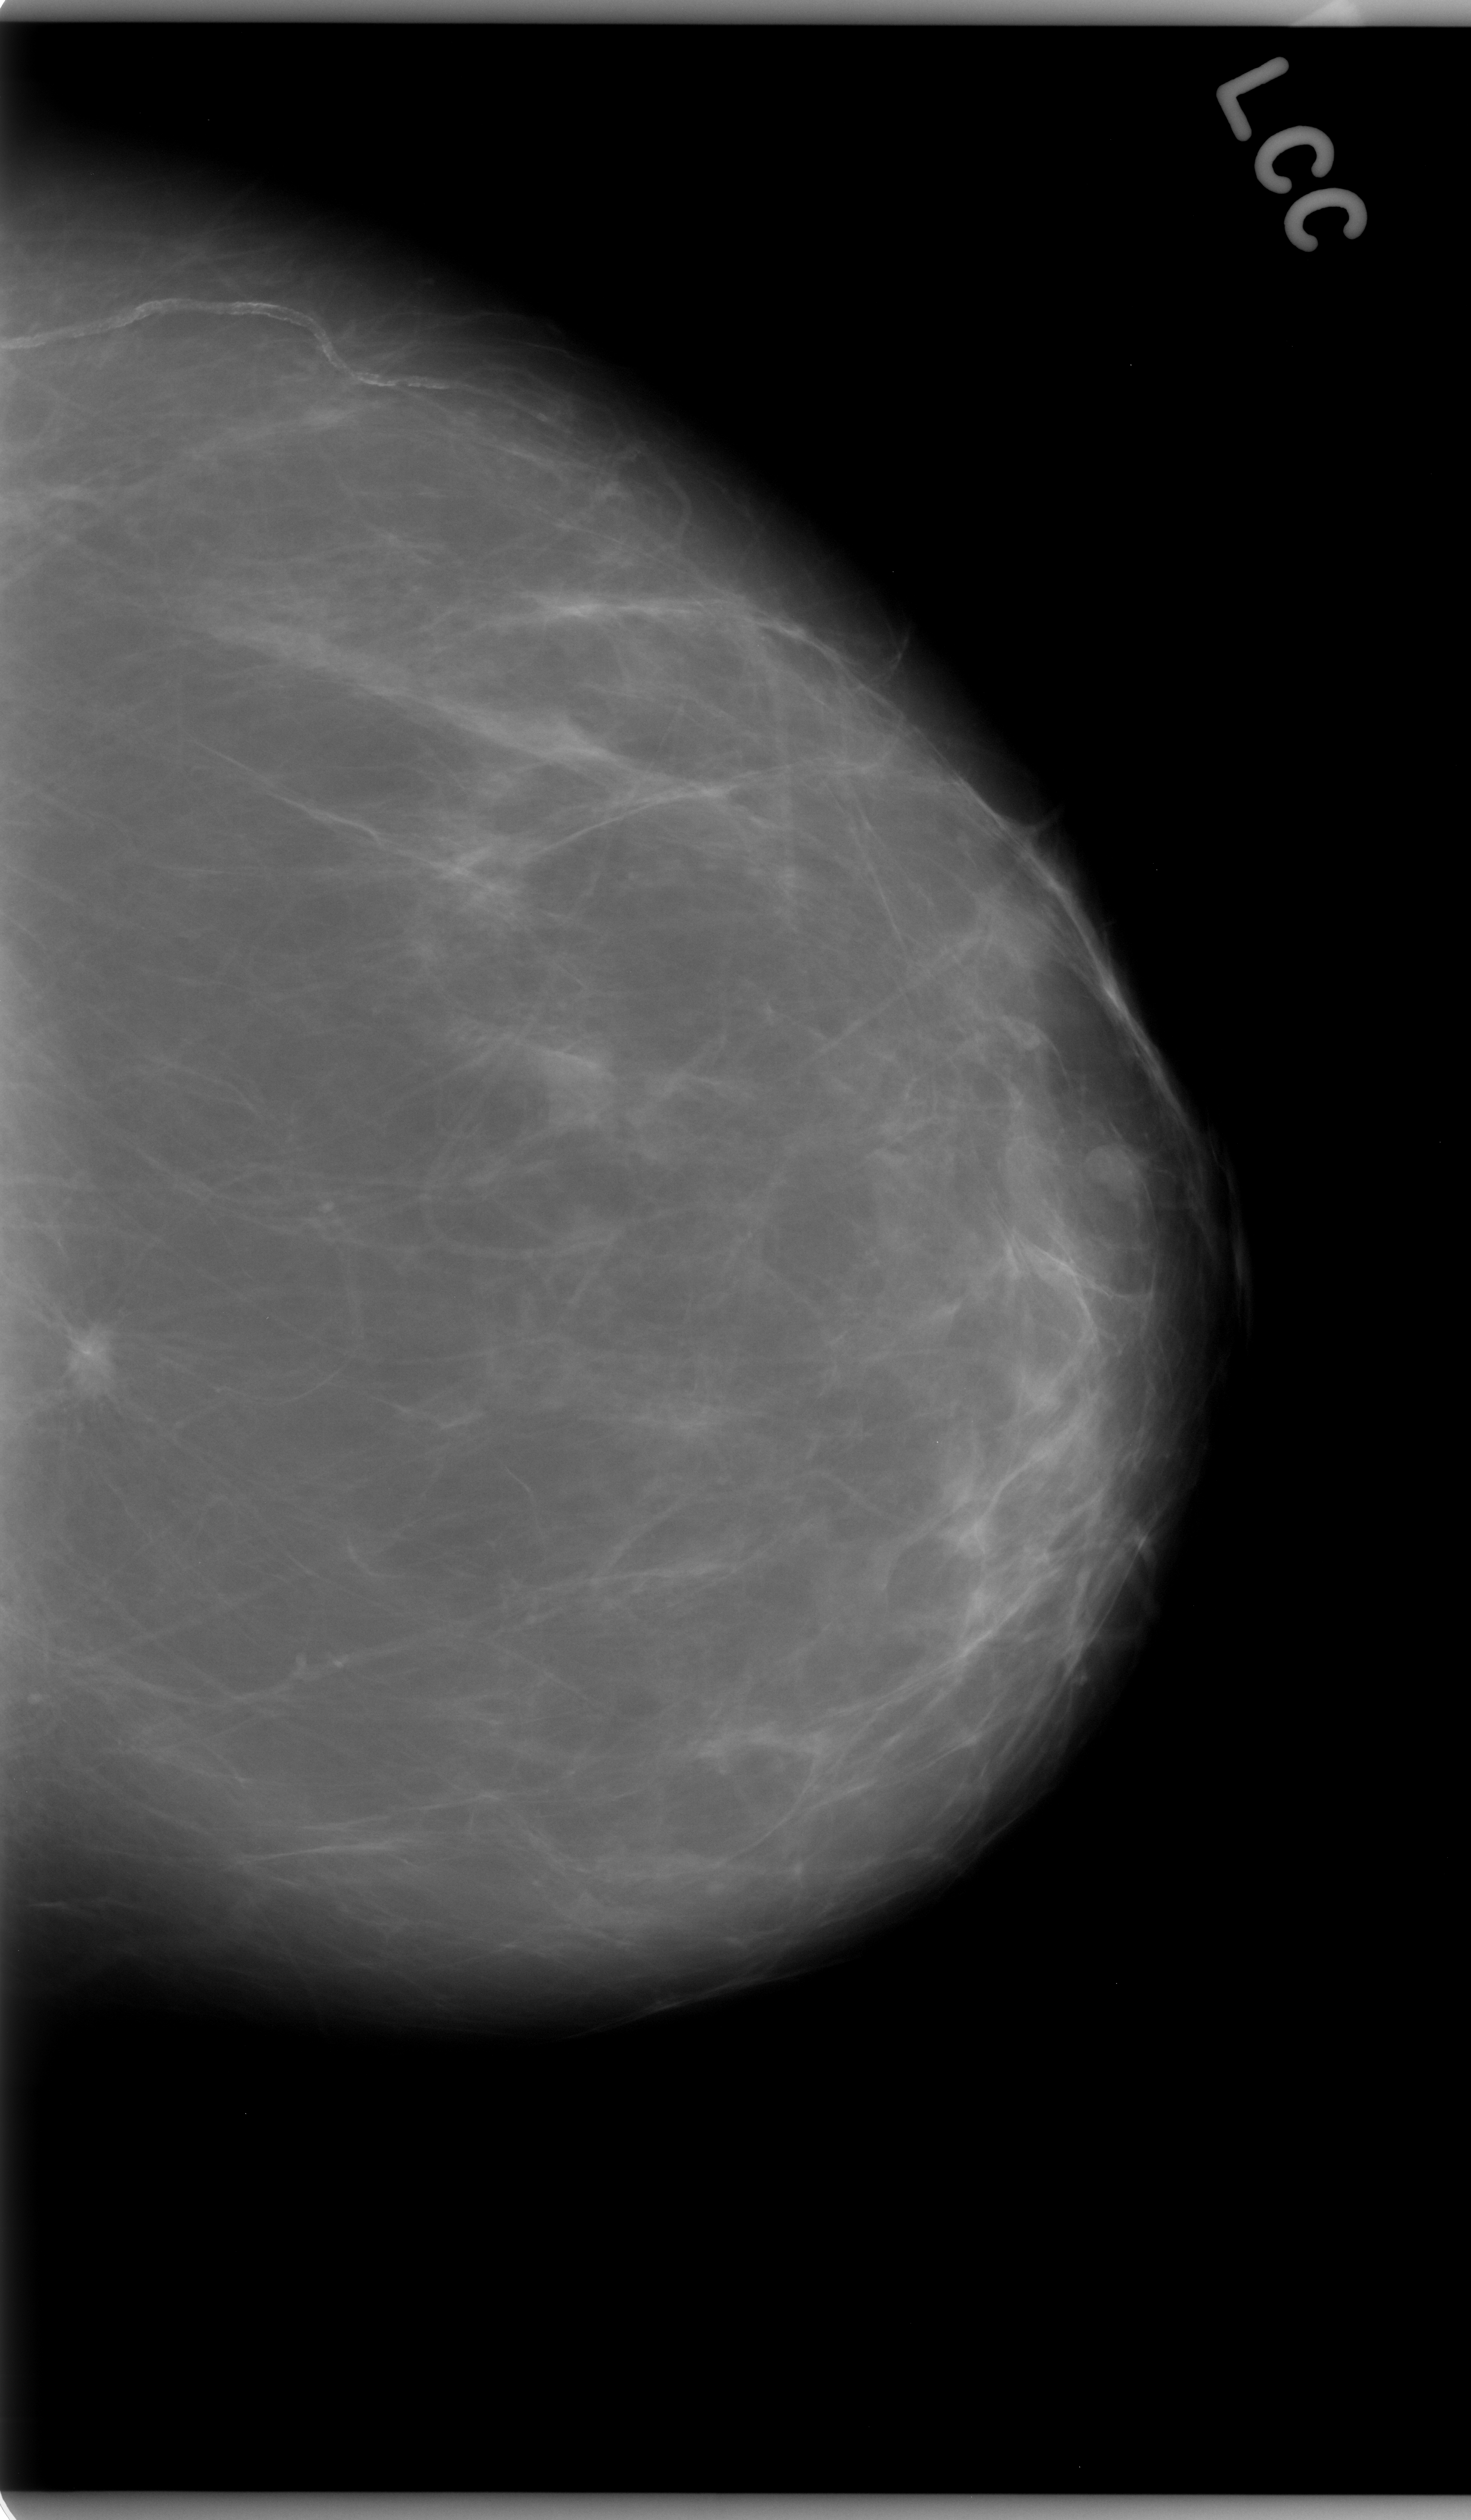
Digitized screen-film mammogram; left breast; craniocaudal (CC) view; breast composition: almost entirely fatty (BI-RADS density category 1 of 4).
Abnormality record for this image: mass, shape irregular, margins spiculated; BI-RADS assessment category 5; pathology result (as recorded, not read from the image): malignant.